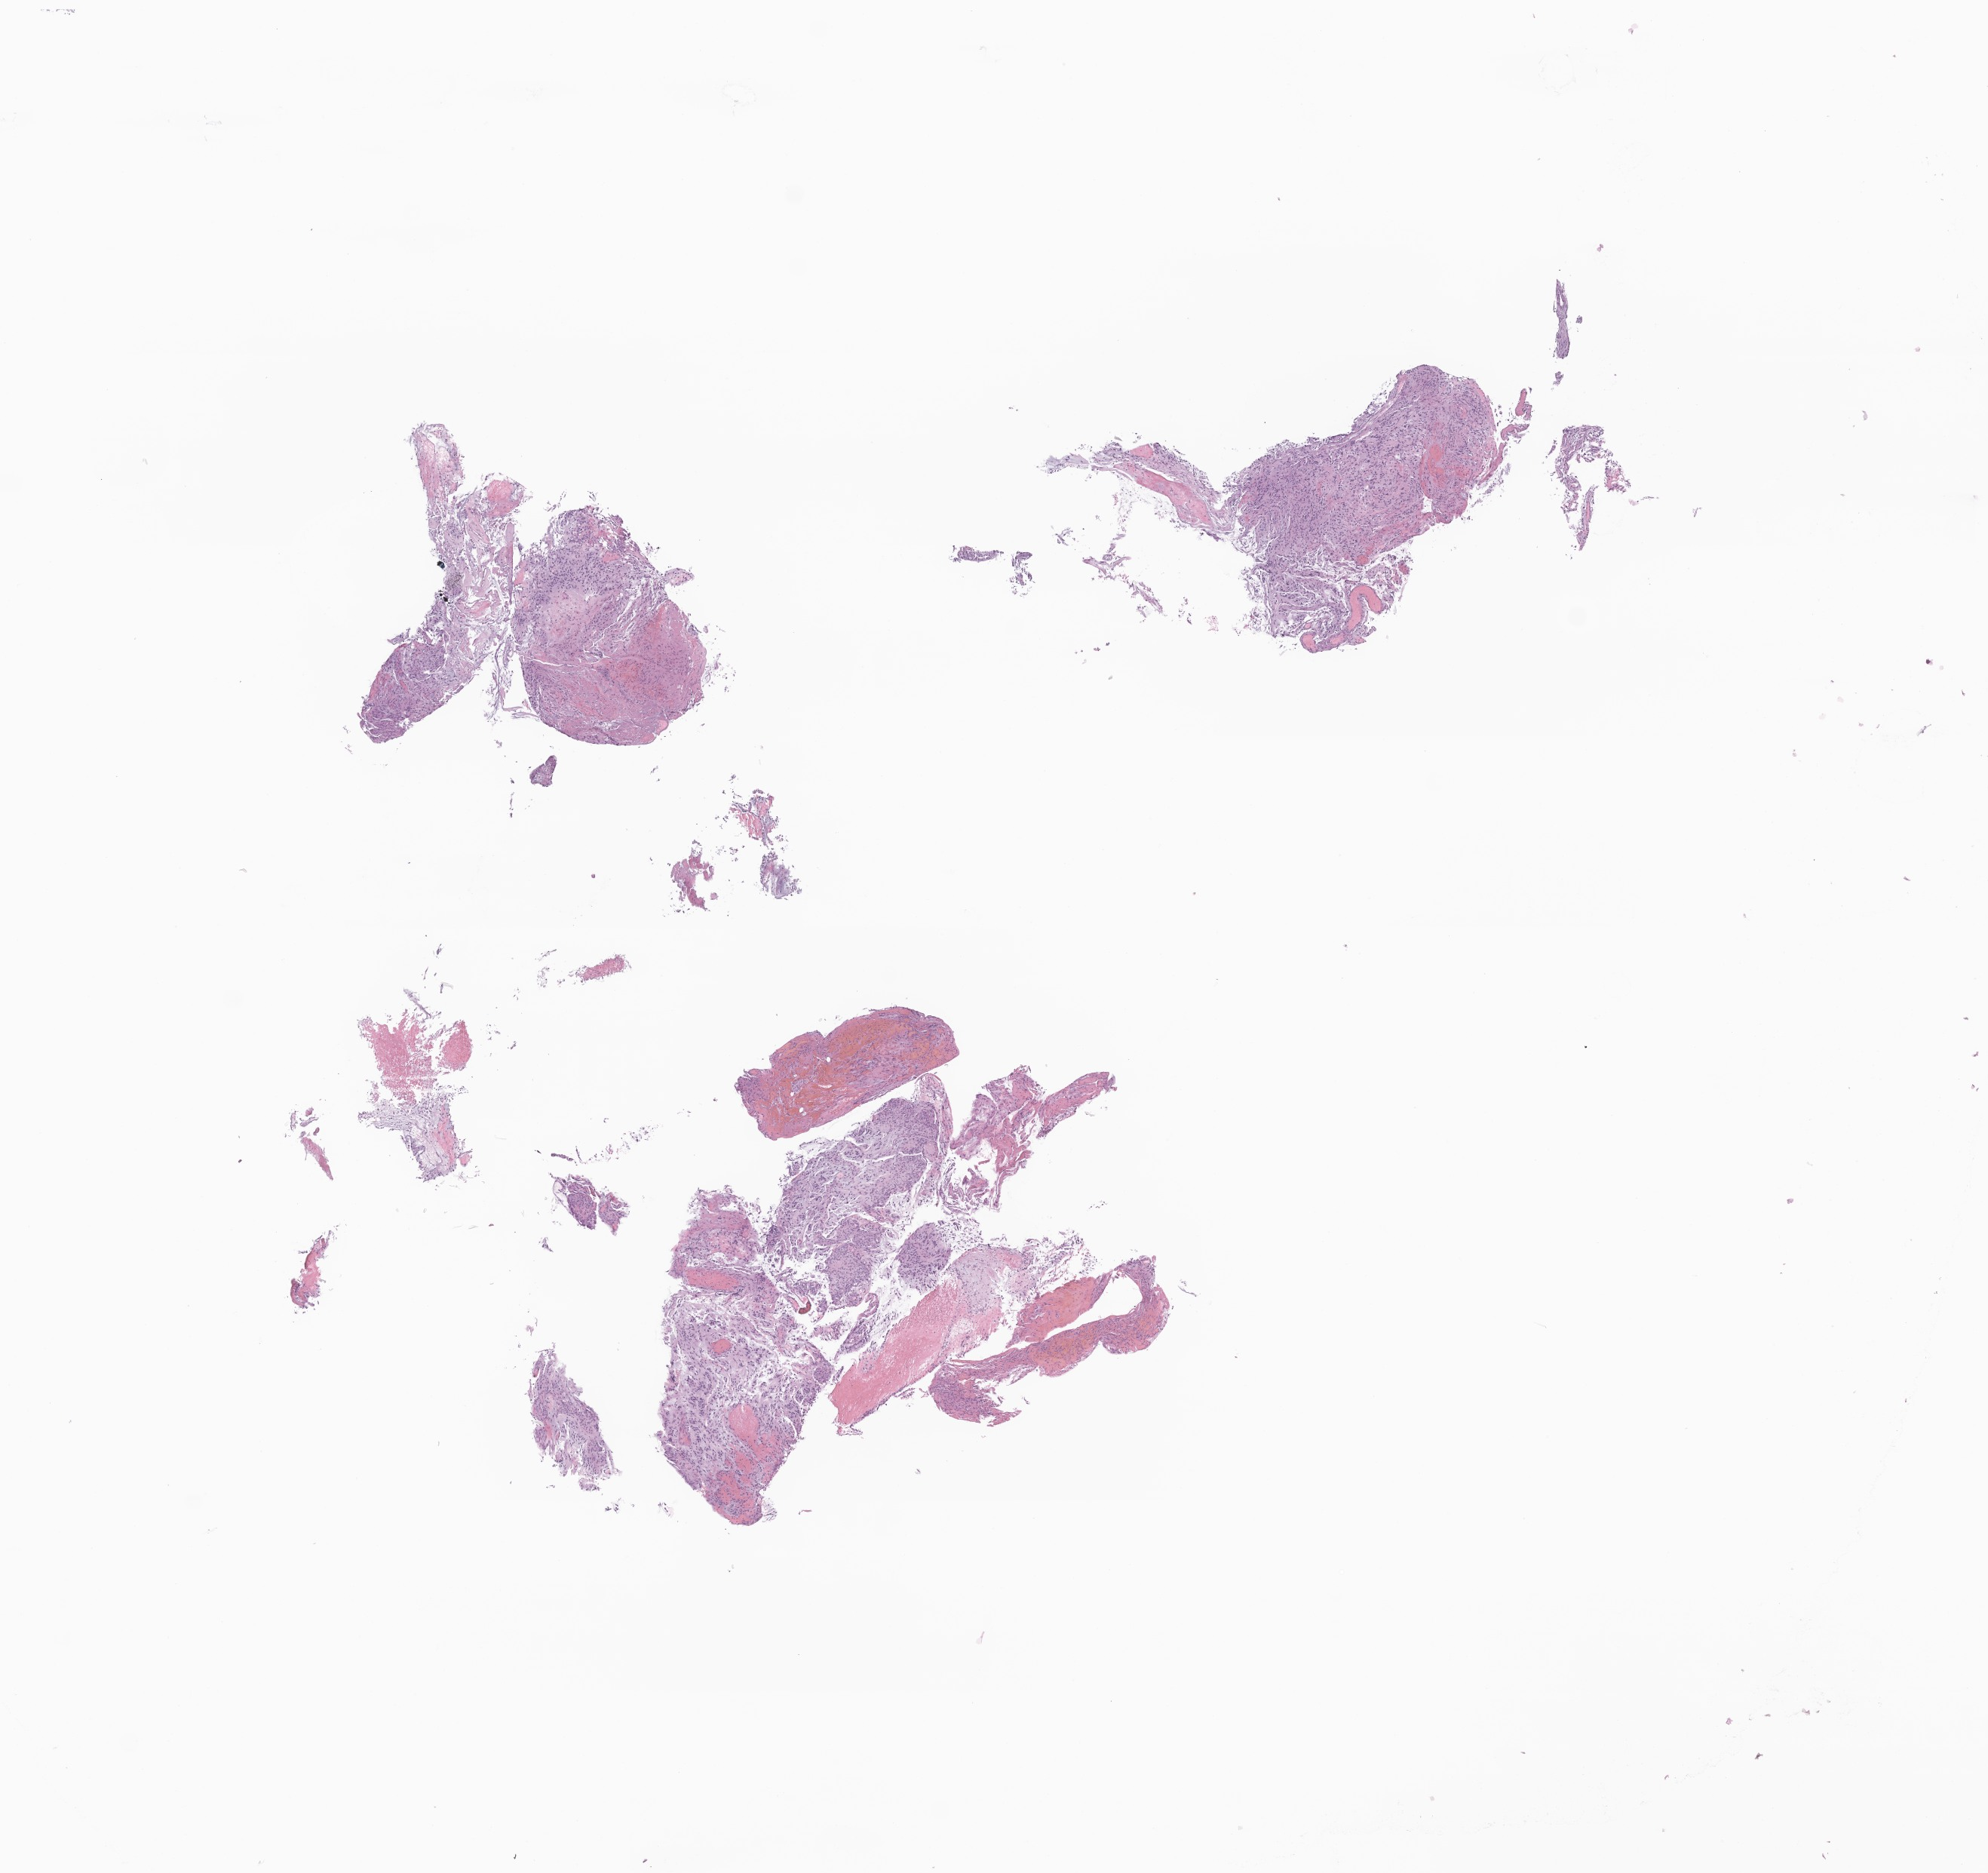
Whole-slide image, H&E stain of tumor tissue from the brain, whole scanned area (about 11.1 x 10.5 mm) shown as a low-resolution overview, FFPE section. Patient male; age 109 months (9 years 1 month).
- diagnosis: Glioma, malignant